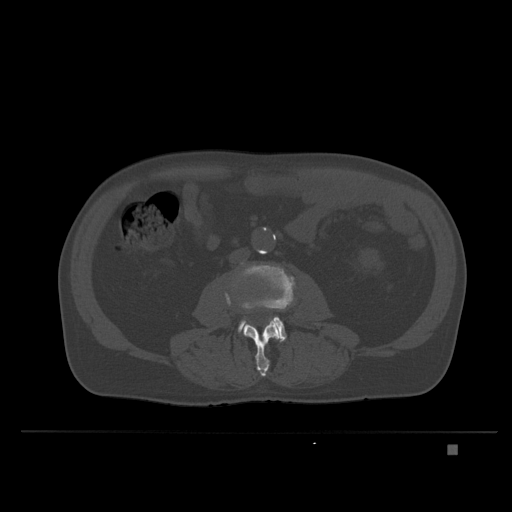
CT including the spine, one axial slice. Slice 88 of 435 in the series (ordered by position). Bone window (W 1800 / L 400 HU). 1.5 mm slice thickness. 512 × 512 image matrix, field of view 434 × 434 mm. Patient: male, 73 years. Case-level facts recorded for this patient, not image findings: primary cancer: skin.
Outlined on this slice (semi-automatically segmented with operator editing):
- L3 vertebra: bounding box (x1, y1, x2, y2) in pixels: (243, 320, 281, 377)
- L4 vertebra: (238, 265, 295, 342)